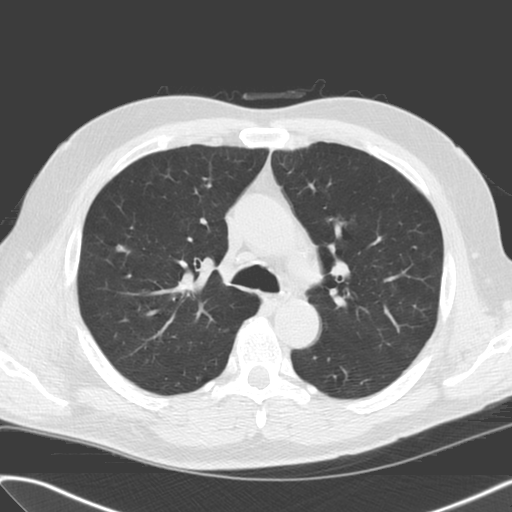
Axial slice from a low-dose chest CT screening exam. Baseline annual screen. Lung window (W 1500 / L -600 HU). Standard (soft-tissue) reconstruction kernel (C). Male participant, aged 61 years at enrolment. Current smoker at enrolment.
Expert reader's lesion annotation, bounding box [x1, y1, x2, y2] px = [104, 235, 136, 265]. Reader record for this screening exam (exam-level; its link to the box is not recorded): non-calcified nodule or mass ≥4 mm, right upper lobe, 6 × 6 mm, smooth margins, soft tissue attenuation. Lung cancer was diagnosed 746 days after this screen: adenocarcinoma, NOS, right upper lobe, stage IIIA (AJCC 6th edition), 13 mm at pathology.